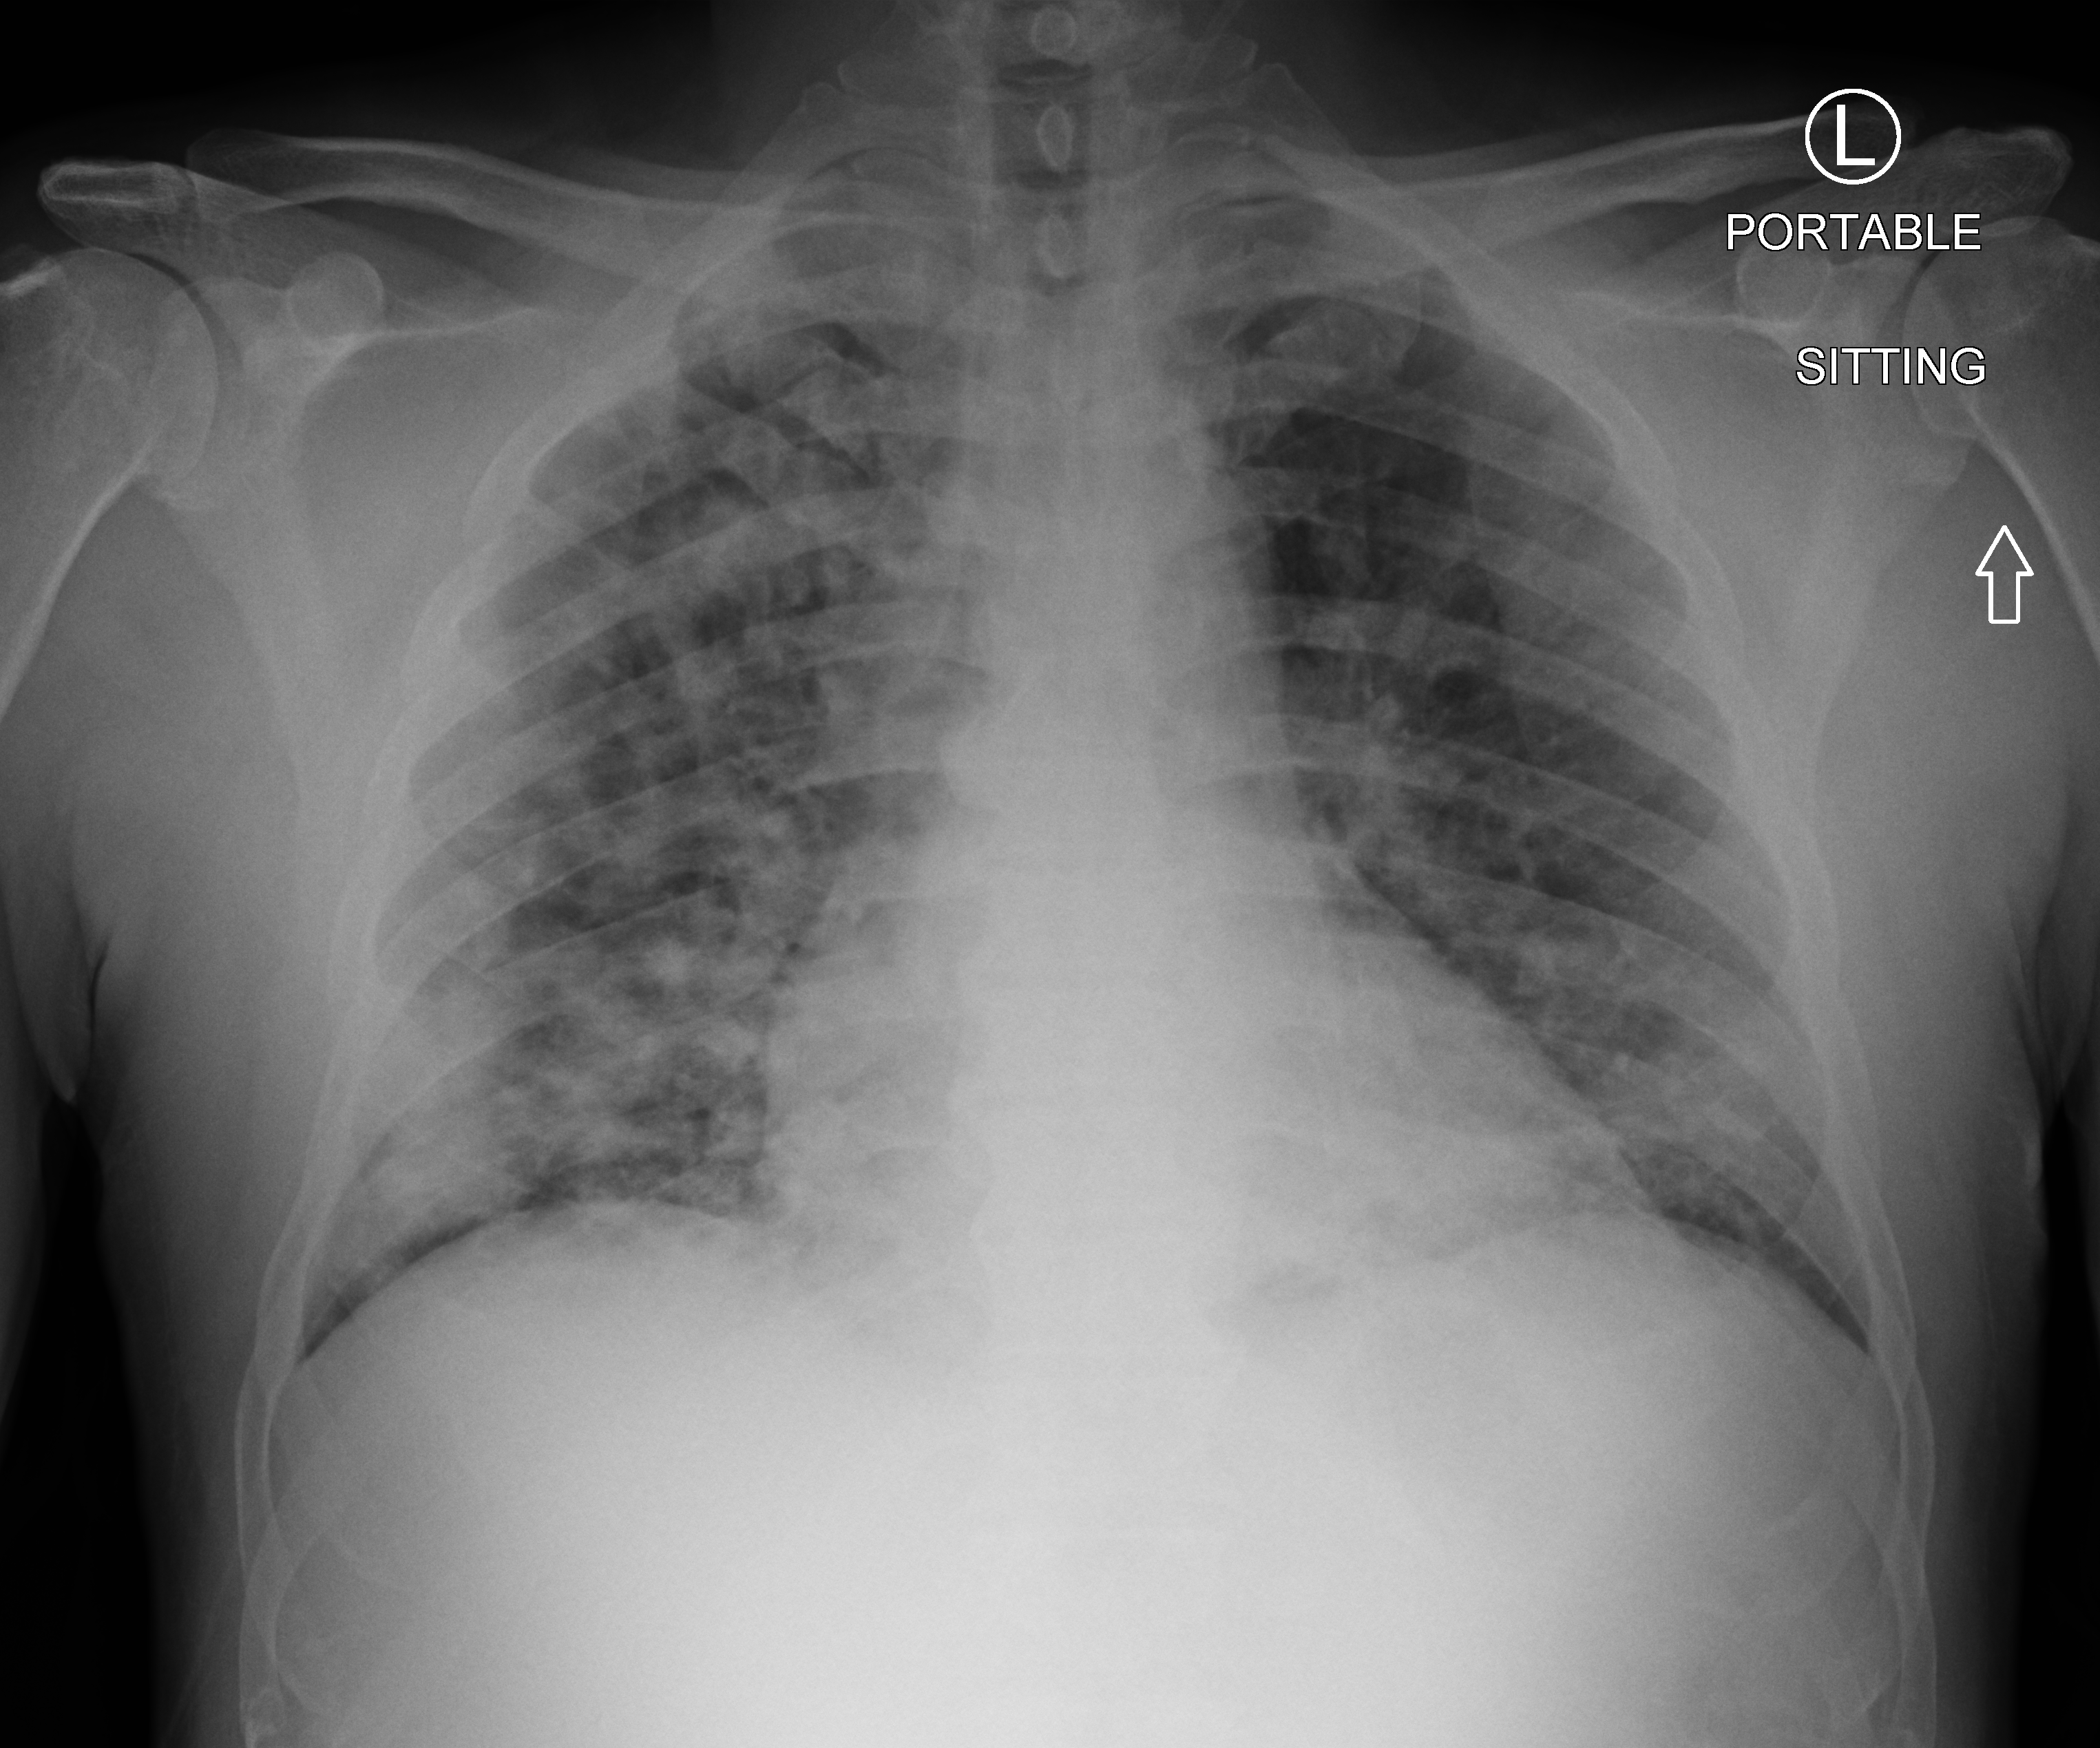
Portable chest radiograph; anteroposterior (AP) projection. Male patient hospitalised with COVID-19, age 18–59 years.
Hospital-stay facts (about this admission, not read from this image; timing relative to this image not recorded): length of hospital stay: 7 days; mechanically ventilated during this hospital stay: no.